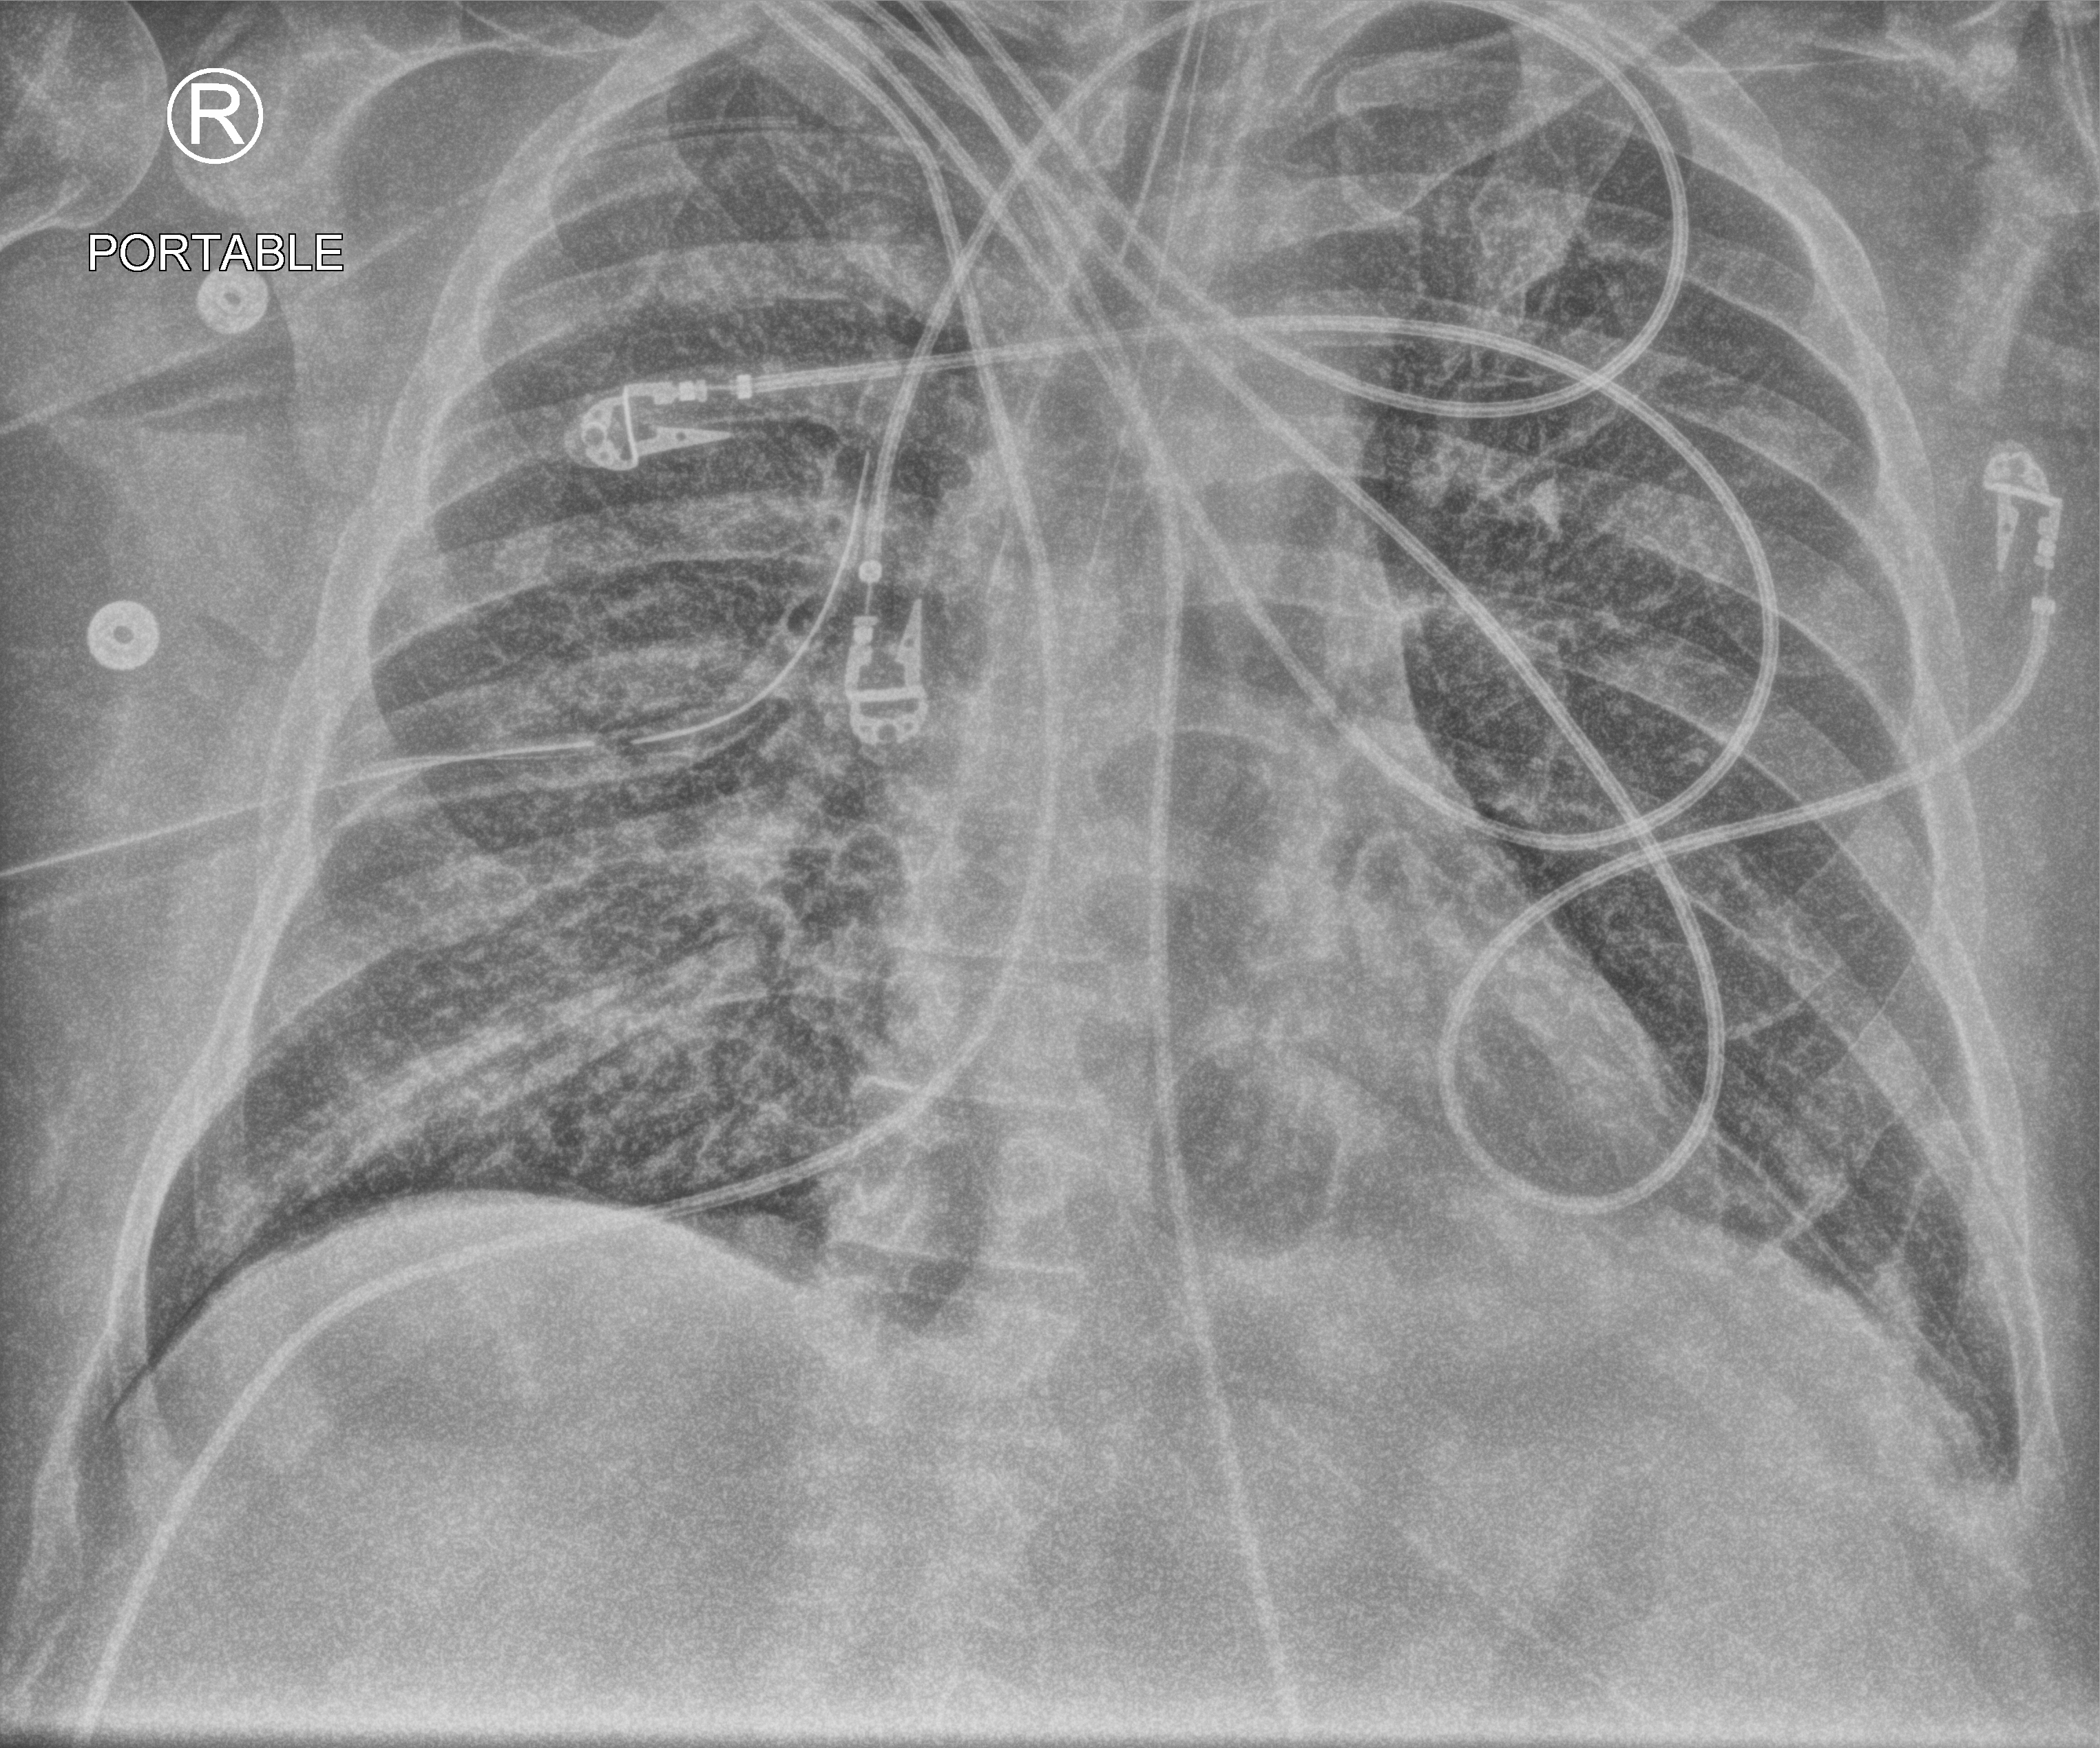
Bedside chest radiograph (computed radiography), anteroposterior (AP) projection. Adult patient hospitalised with COVID-19, age 18–59 years.
Hospital-stay facts (about this admission, not read from this image; timing relative to this image not recorded):
- mechanically ventilated during this hospital stay: yes
- length of hospital stay: 26 days
- admitted to intensive care during this hospital stay: yes